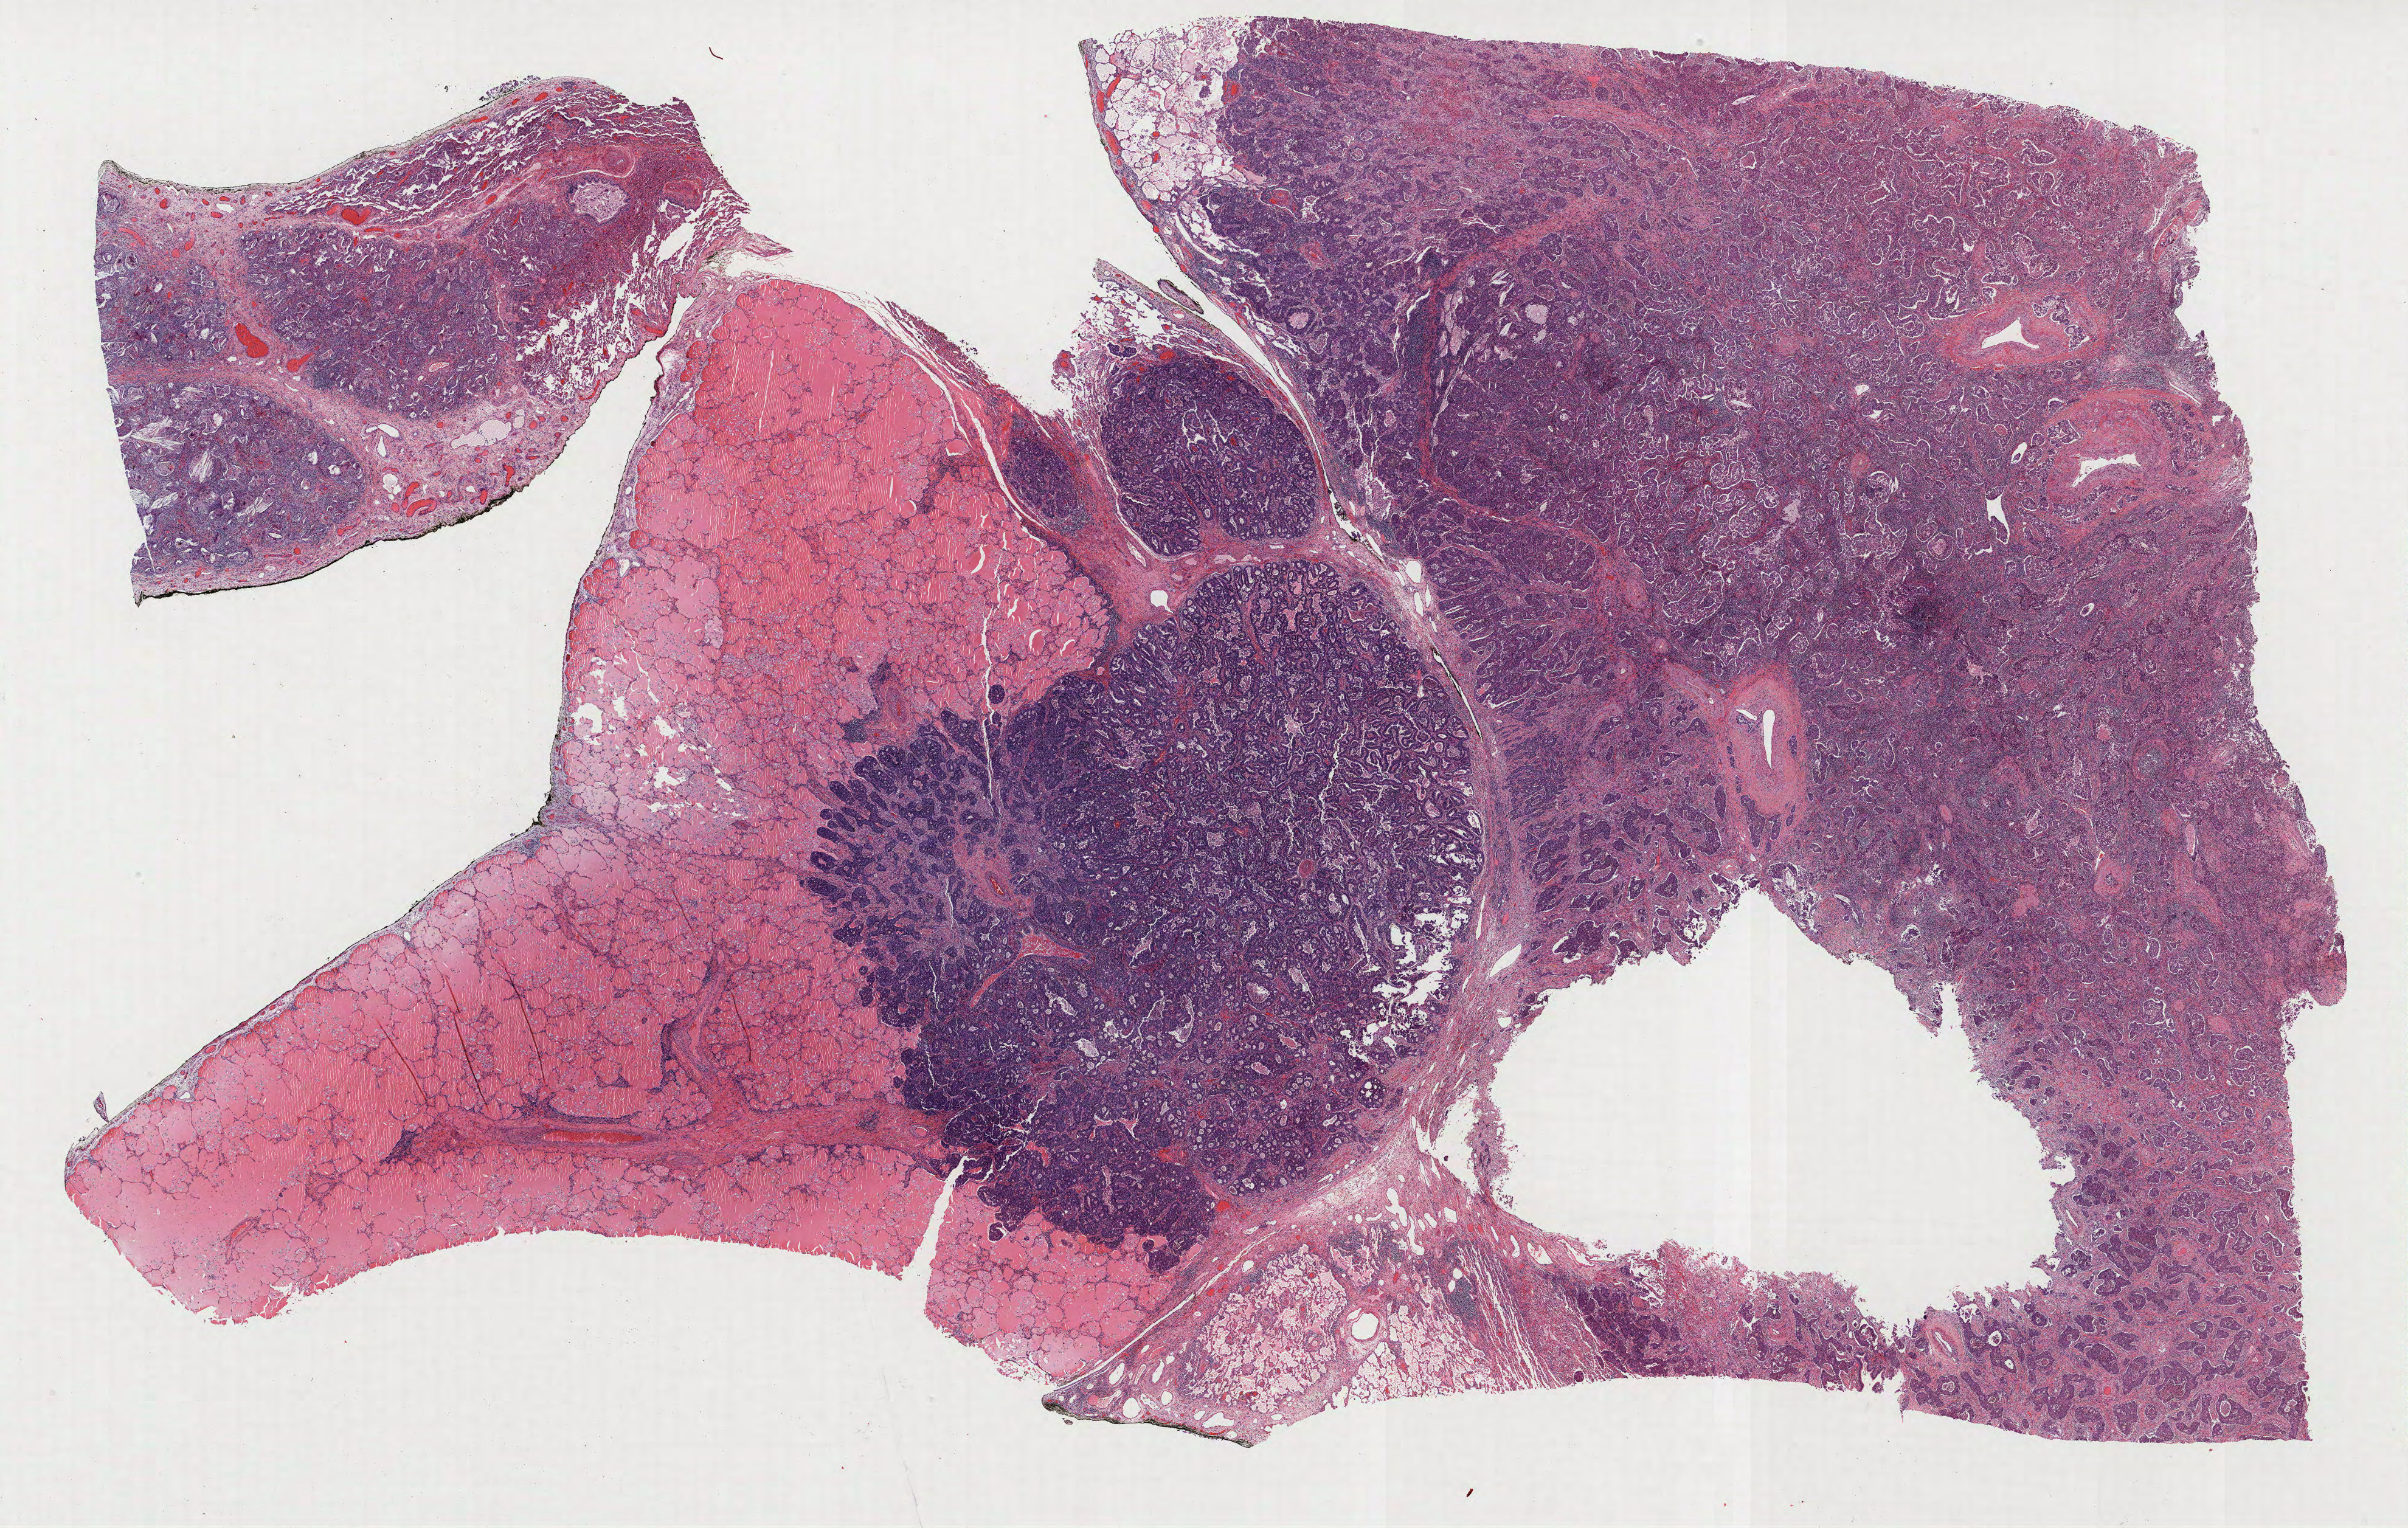
H&E whole-slide image — low-resolution overview of the scanned area, about 31.7 x 20.1 mm, formalin-fixed paraffin-embedded (FFPE) section, lung tissue. Female patient, aged 66 at enrolment. Former smoker at enrolment. Grade: moderately differentiated (G2).
Stage (AJCC 6th edition): IV. Participant's lung-cancer diagnosis: Adenocarcinoma, NOS. Primary tumour location (clinical record): right lower lobe. ICD-O-3 topography: lower lobe of lung (C34.3). Tumour size (pathology): 60 mm.